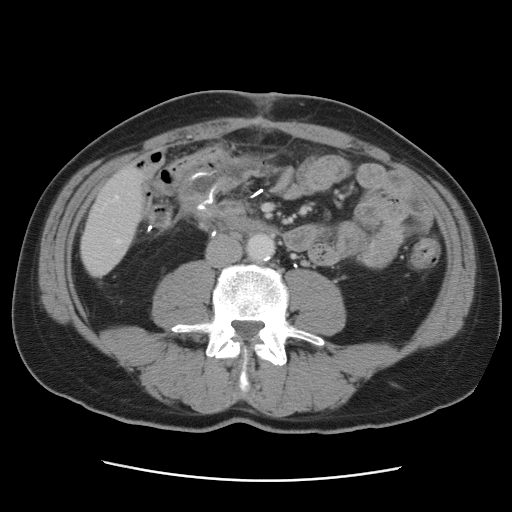
Contrast-enhanced abdominal CT, one axial slice; slice 13 of 89 in the series (ordered by position); intravenous contrast given; soft-tissue window (W 400 / L 40 HU); 5 mm slice thickness; 512 × 512 image matrix. Male patient, age 59 years. Case-level facts recorded for this patient, not image findings: diagnosis: colorectal cancer liver metastases, imaged before liver resection; multiple liver metastases: yes; largest metastasis: 0.6 cm; disease in both lobes: yes.
Structures marked on this image (manually delineated by an expert):
- hepatic veins: bounding box (x1, y1, x2, y2) in pixels: (115, 196, 121, 243)
- liver: (82, 167, 145, 275)
- planned liver remnant (the part of the liver to remain after resection): (82, 167, 144, 258)